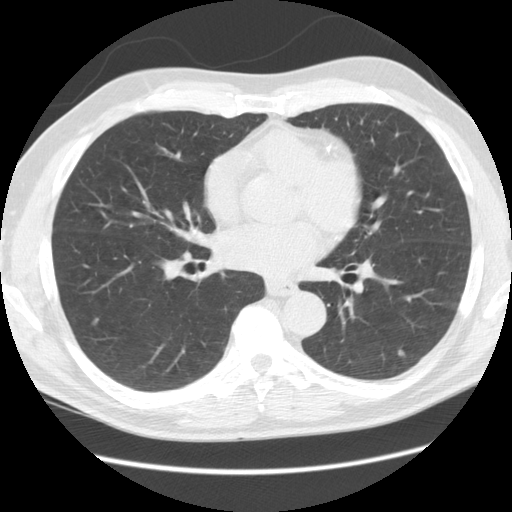
Low-dose screening chest CT, one axial slice; slice 48 of 111 in the series (ordered by position); 120 kVp; lung window (W 1500 / L -600 HU); 2.5 mm slice thickness; 512 × 512 image matrix, field of view 370 × 370 mm.
Structures marked on this image (expert manual segmentation):
- lesion 3 (nodule, lower lobe of right lung): bounding box [x1, y1, x2, y2] px = [93, 317, 99, 323]